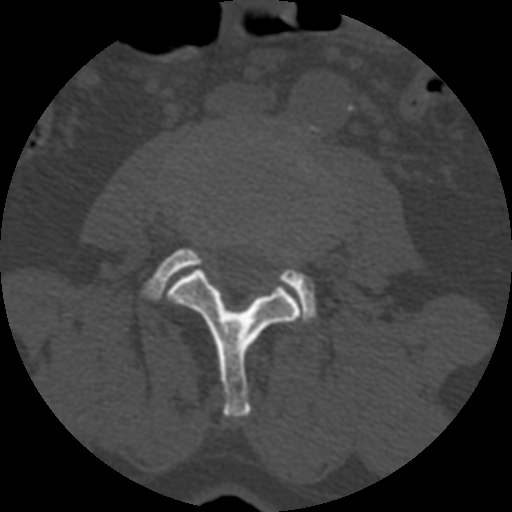
CT including the spine, one axial slice. Slice 297 of 399 in the series (ordered by position). 120 kVp. Bone window (W 1800 / L 400 HU). 1.25 mm slice thickness. 512 × 512 image matrix, field of view 160 × 160 mm. Patient age 71 years. Case-level facts recorded for this patient, not image findings: primary cancer: prostate.
Structures marked on this image (semi-automatically segmented with operator editing):
- L3 vertebra: box from (x=167, y=238) to (x=305, y=419) px
- L4 vertebra: (x=141, y=248)–(x=317, y=322)